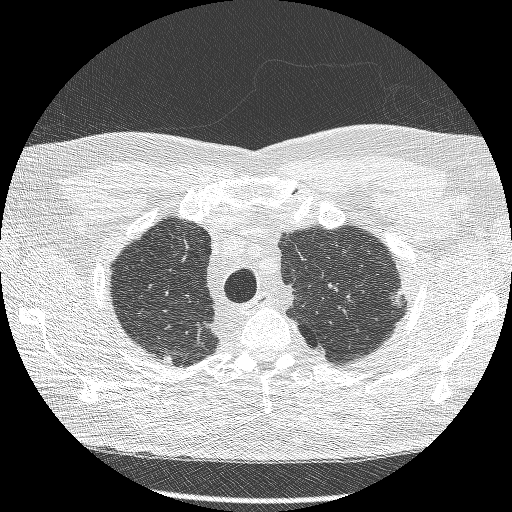
Chest CT (low-dose screening protocol), one axial image; second screening round (one year after baseline); lung window (W 1500 / L -600 HU); lung (sharp) reconstruction kernel (BONE); 512 × 512 image matrix. Male, age 66 years at enrolment. Current smoker at enrolment.
Expert reader's lesion annotation, bounding box [x1, y1, x2, y2] px = [381, 277, 418, 323]. The exam's reader record, not a measurement of the box and not confirmed to be the same lesion: non-calcified nodule or mass ≥4 mm, right lower lobe, 40 × 19 mm, spiculated (stellate) margins, soft tissue attenuation, pre-existing on the prior screen: yes; interval growth: no. Note: the box lies in the patient's left hemithorax on this image, whereas the reader's record names the right lung; they may be different findings. Official screen result: negative screen, minor abnormalities not suspicious for lung cancer. Lung cancer was diagnosed 554 days after this screen: adenocarcinoma, NOS, left upper lobe, poorly differentiated (G3), stage IB (AJCC 6th edition), 16 mm at pathology.